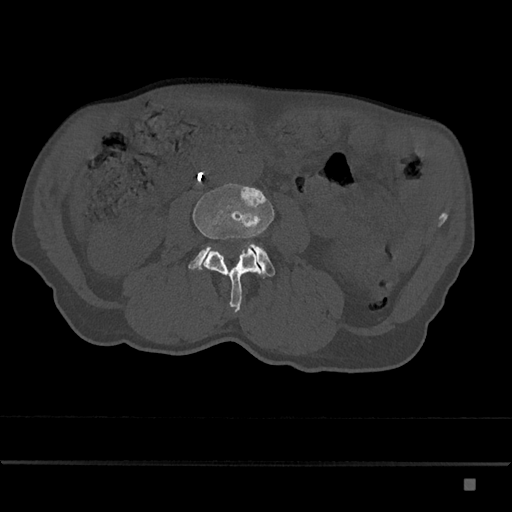
CT including the spine, one axial slice. Slice 383 of 797 in the series (ordered by position). Reconstruction kernel Br40s/3. 120 kVp. Bone window (W 1800 / L 400 HU). 0.5 mm slice thickness. 512 × 512 image matrix, field of view 390 × 390 mm. Male patient, age 72 years. Case-level facts recorded for this patient, not image findings: primary cancer: prostate.
Annotated regions visible in this slice (semi-automatically segmented with operator editing):
- L3 vertebra: bounding box [x1, y1, x2, y2] px = [192, 183, 274, 313]
- L4 vertebra: [188, 243, 275, 278]